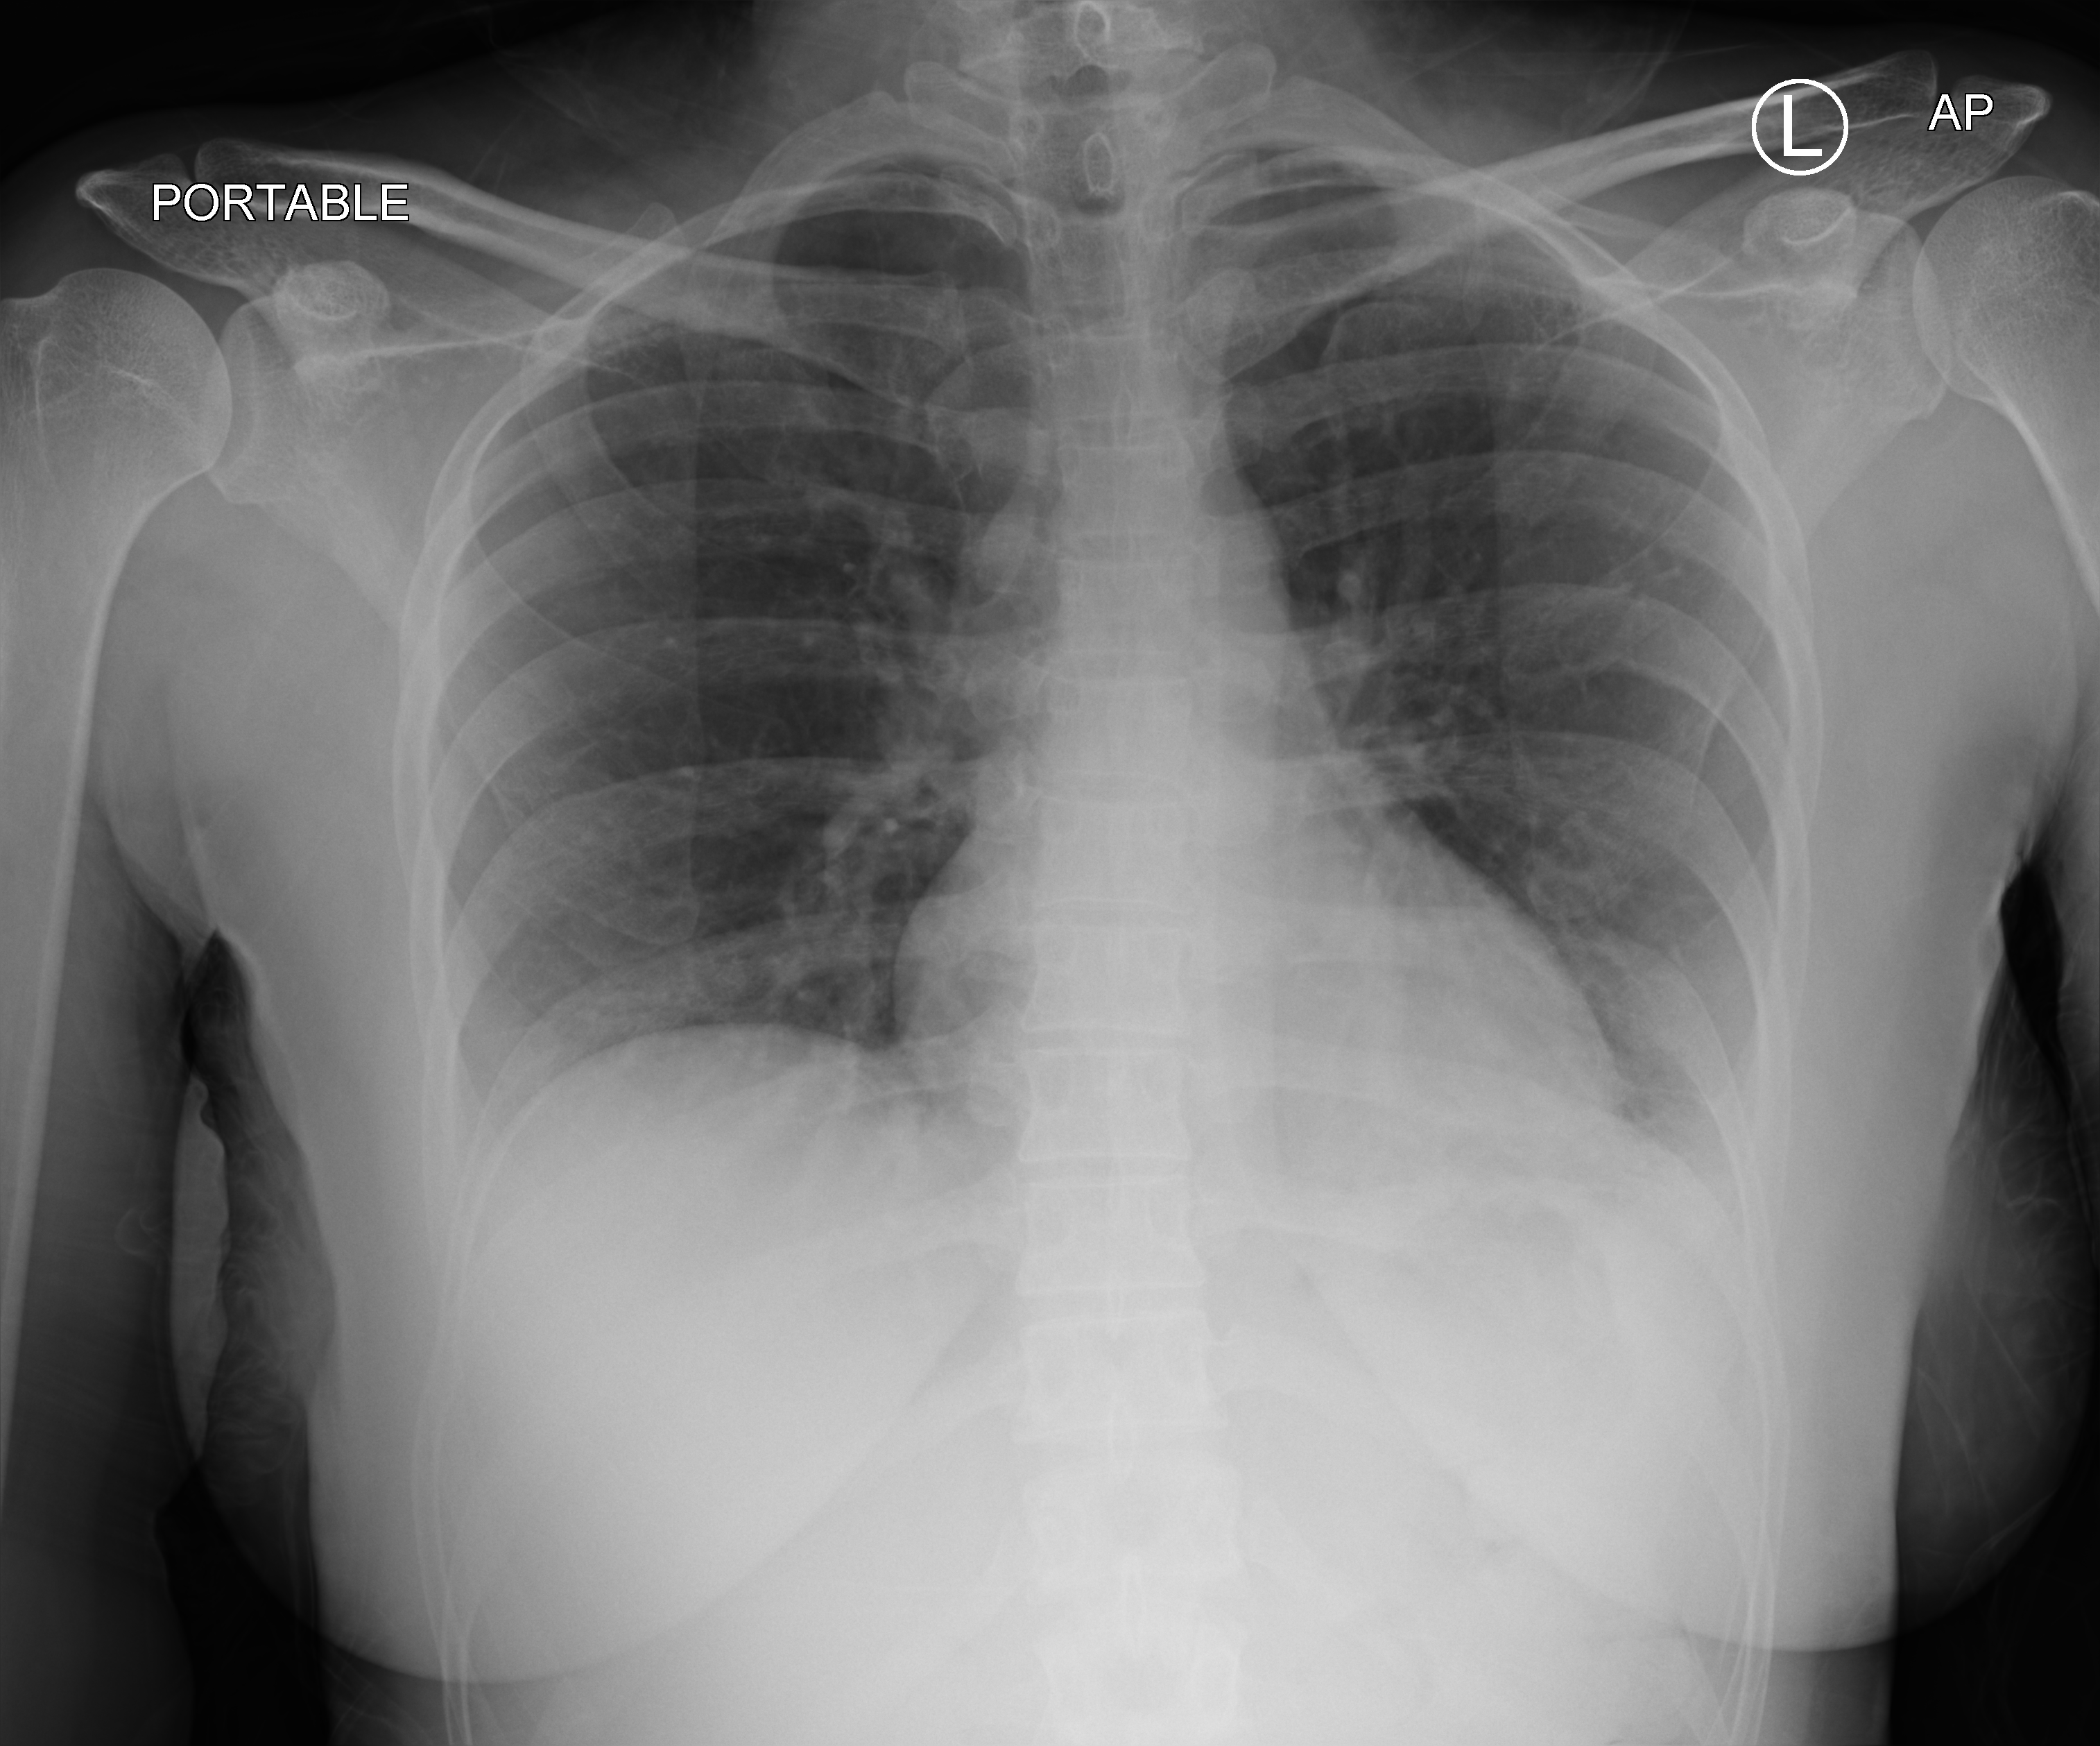
Bedside chest radiograph (computed radiography), anteroposterior (AP) projection. Patient hospitalised with COVID-19; female, aged 18–59 years.
Admission-level facts for this patient (not findings on this image; timing relative to this image not recorded): mechanically ventilated during this hospital stay: no; admitted to intensive care during this hospital stay: no; length of hospital stay: 2 days.